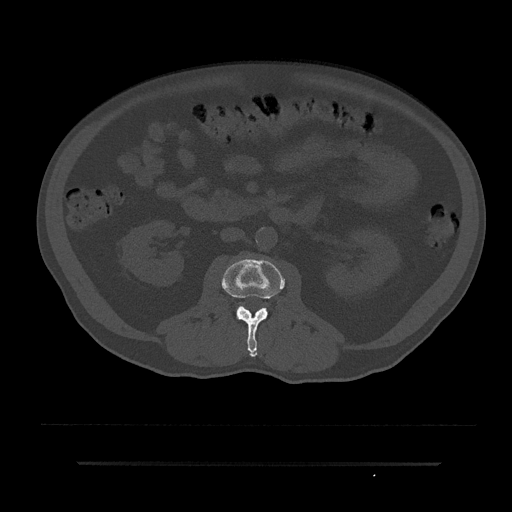
CT including the spine, one axial slice. Slice 54 of 797 in the series (ordered by position). Reconstruction kernel Br40s/3. Bone window (W 1800 / L 400 HU). 0.5 mm slice thickness. 512 × 512 image matrix, field of view 464 × 464 mm. Male patient, age 59 years. Case-level facts recorded for this patient, not image findings: primary cancer: bile ducts; vertebrae with lytic lesions (as recorded): T10.
Structures marked on this image (semi-automatically segmented with operator editing):
- L2 vertebra: box from (x=221, y=257) to (x=285, y=357) px